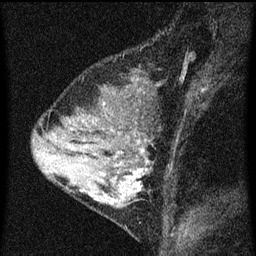
Breast MRI (dynamic contrast-enhanced), one sagittal slice. Position 25 of 60 along the scan axis. Dynamic contrast-enhanced series, image 2 of 3 at this slice position (ordered by acquisition). 1.5 T. TE 4.2 ms, TR 8 ms. 2 mm slice thickness. 256 × 256 image matrix. Female patient, age 33 years.
Structures marked on this image (semi-automatically segmented with operator editing):
- analysis volume of interest (the breast-tissue region the enhancement analysis was run in; not a lesion): bounding box [x1, y1, x2, y2] px = [67, 118, 161, 213]
- tumour enhancement mask (voxels above the 70 % enhancement threshold inside the analysis volume of interest): [89, 134, 149, 201]